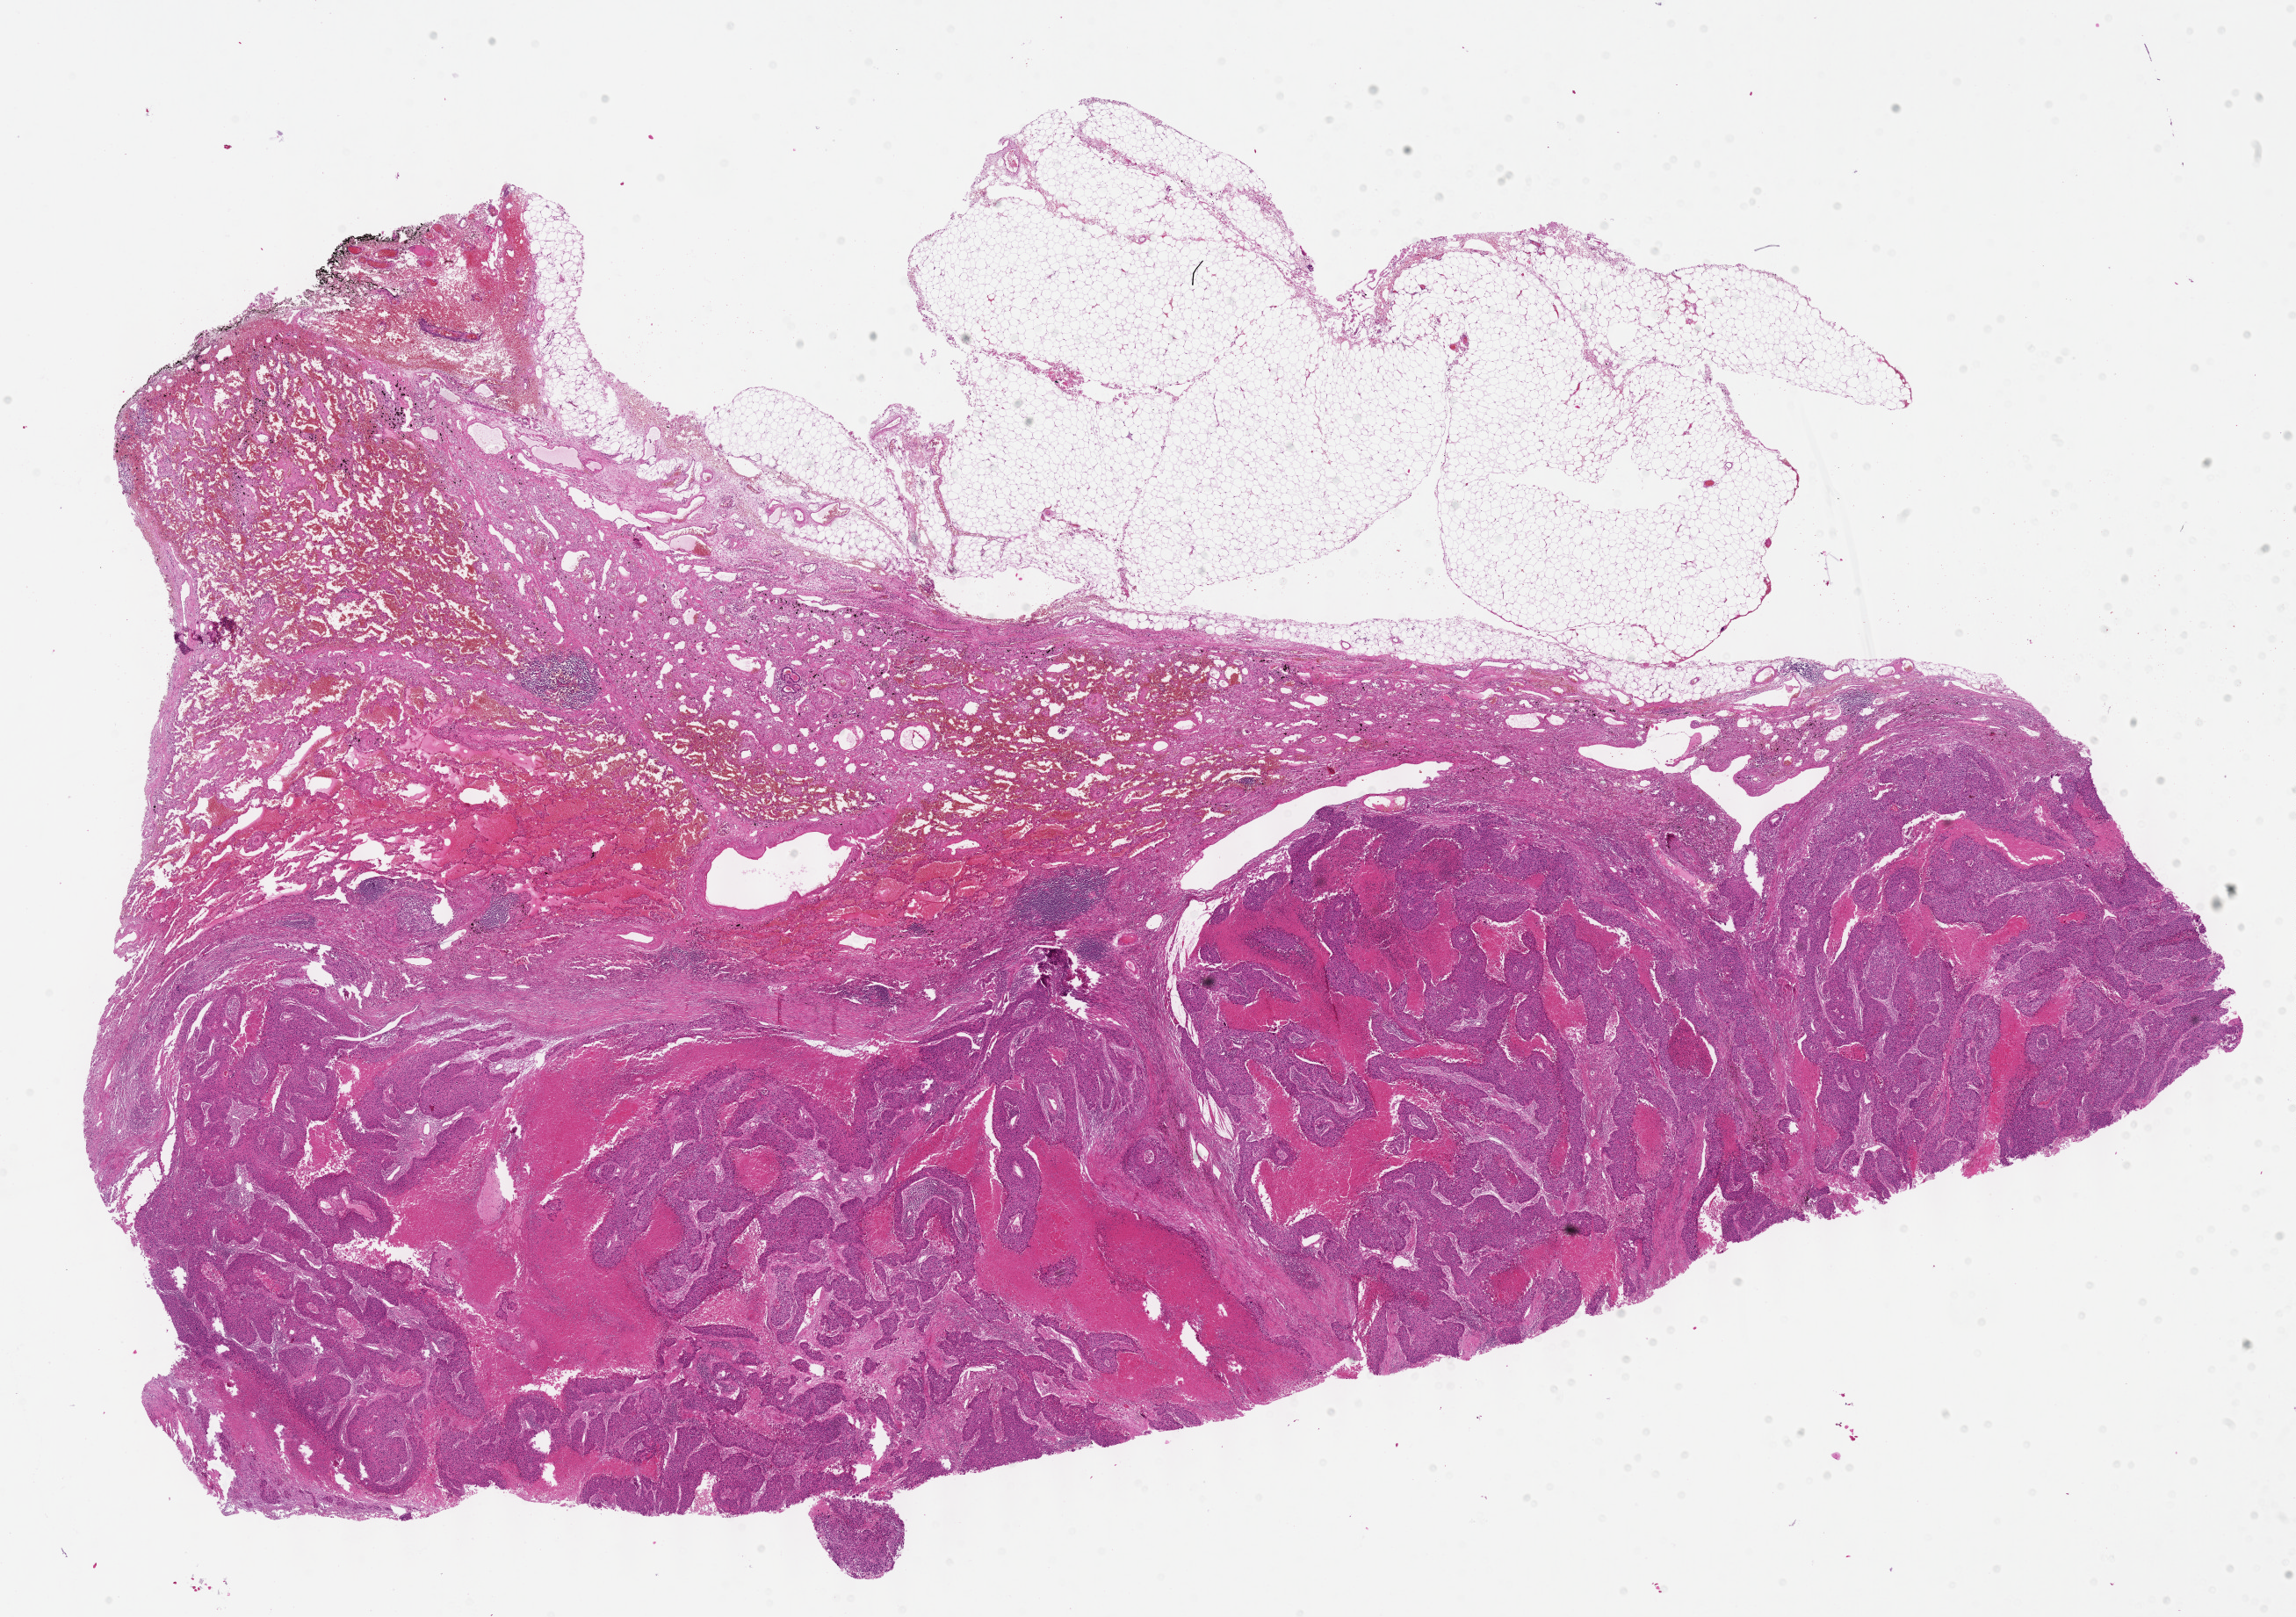
Whole-slide histology image, H&E-stained, whole scanned area (about 21.1 x 14.9 mm, slide scanned at 40x) shown as a low-resolution overview; FFPE section; sample: primary tumour, lung. Male patient; age at initial diagnosis 73 years.
AJCC pathologic stage: IIA (7th edition). Histologic diagnosis: Squamous cell carcinoma, NOS (upper lobe, lung).